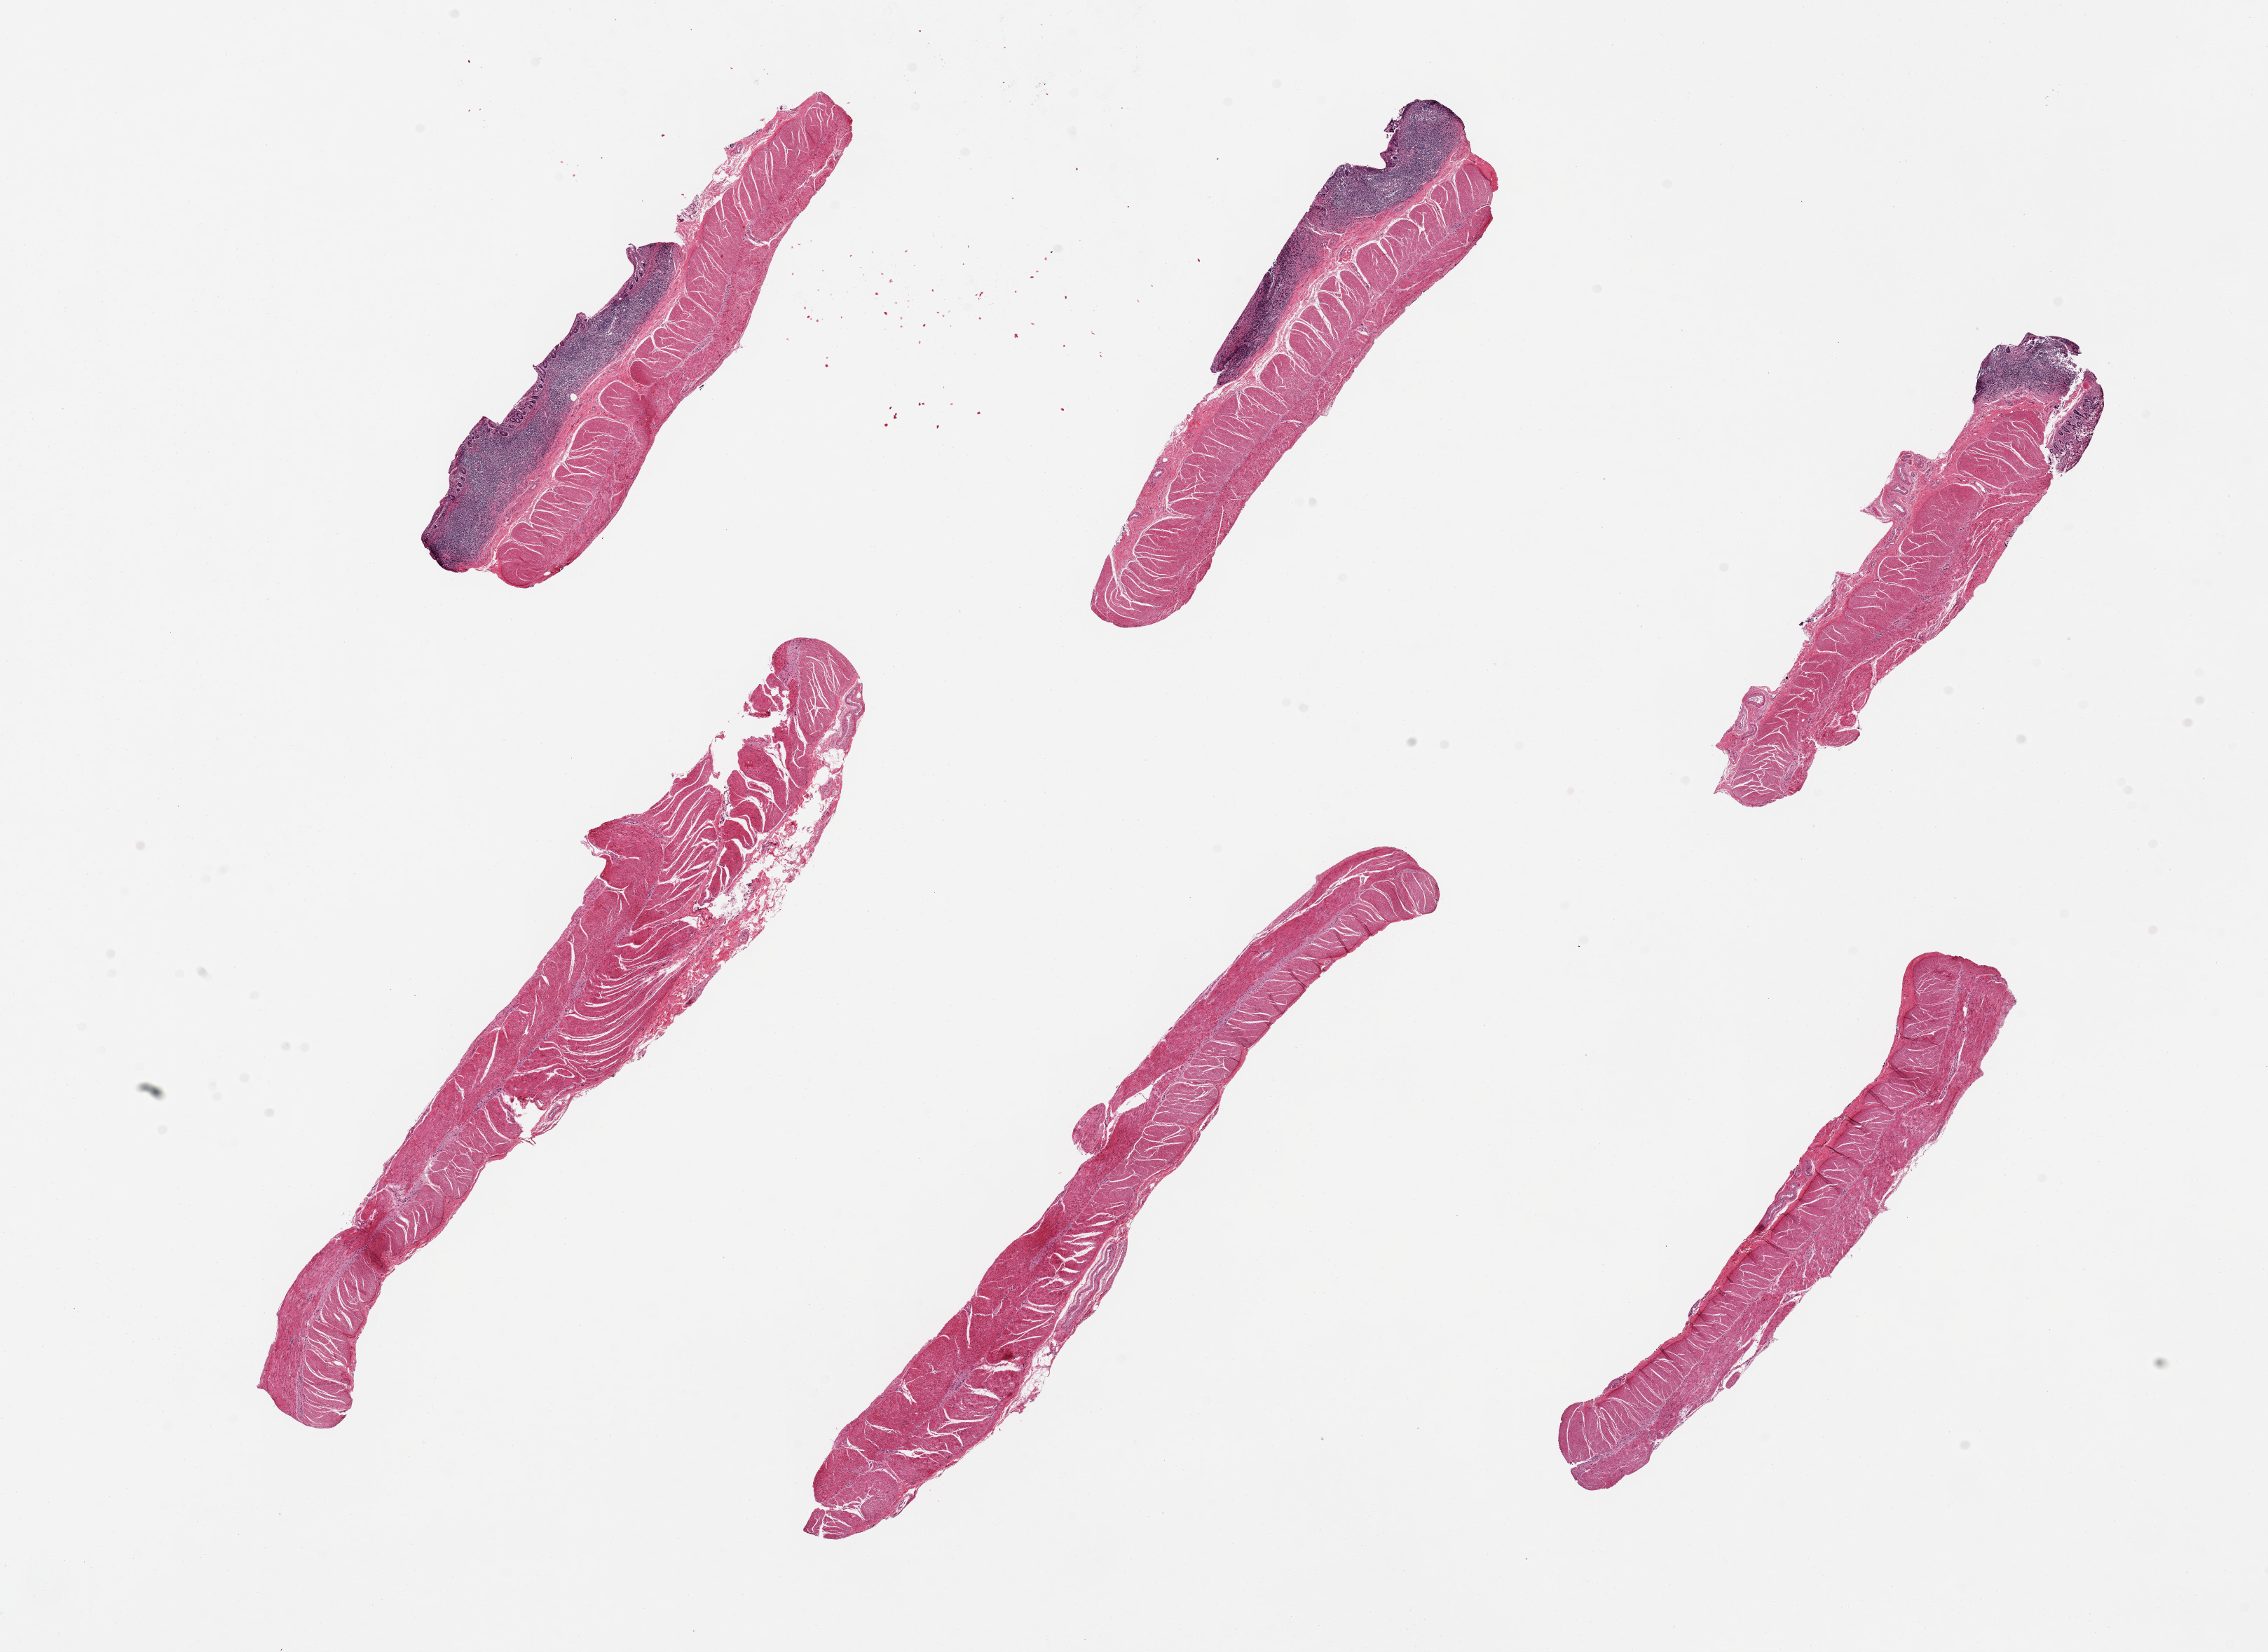
H&E whole-slide image, shown as a low-resolution overview of the whole scanned area (about 25.6 x 18.6 mm, from a 20x scan); PAXgene-fixed, paraffin-embedded tissue; section of ileum (target tissue); tissue donor sample. Female donor.
* review note (as recorded): 6 pieces, up to 11x2mm; actually ileum, lymphoid elements are ~15% of specimen